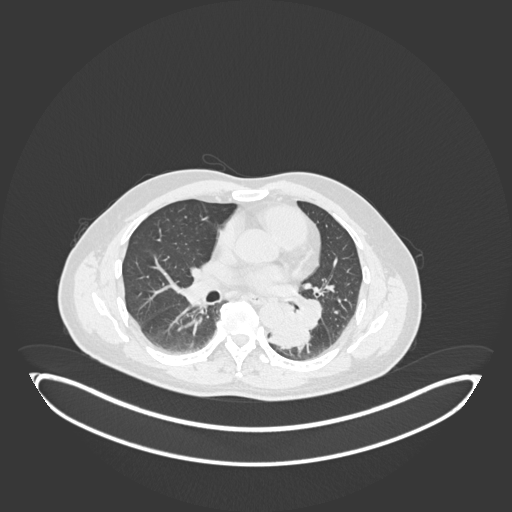
Chest CT, one axial slice. Position 102 of 258 along the scan axis. Reconstruction kernel B30f. 120 kVp. Lung window (W 1500 / L -600 HU). 512 × 512 image matrix, field of view 500 × 500 mm. Male patient, age 54 years. From the clinical record (not read from this slice): clinical TNM (as recorded): T3 N0 M0.
Annotated regions visible in this slice (rectangle marked by the reading radiologist):
- lung tumour (recorded histology: squamous cell carcinoma): bounding box [x1, y1, x2, y2] px = [268, 314, 312, 357]